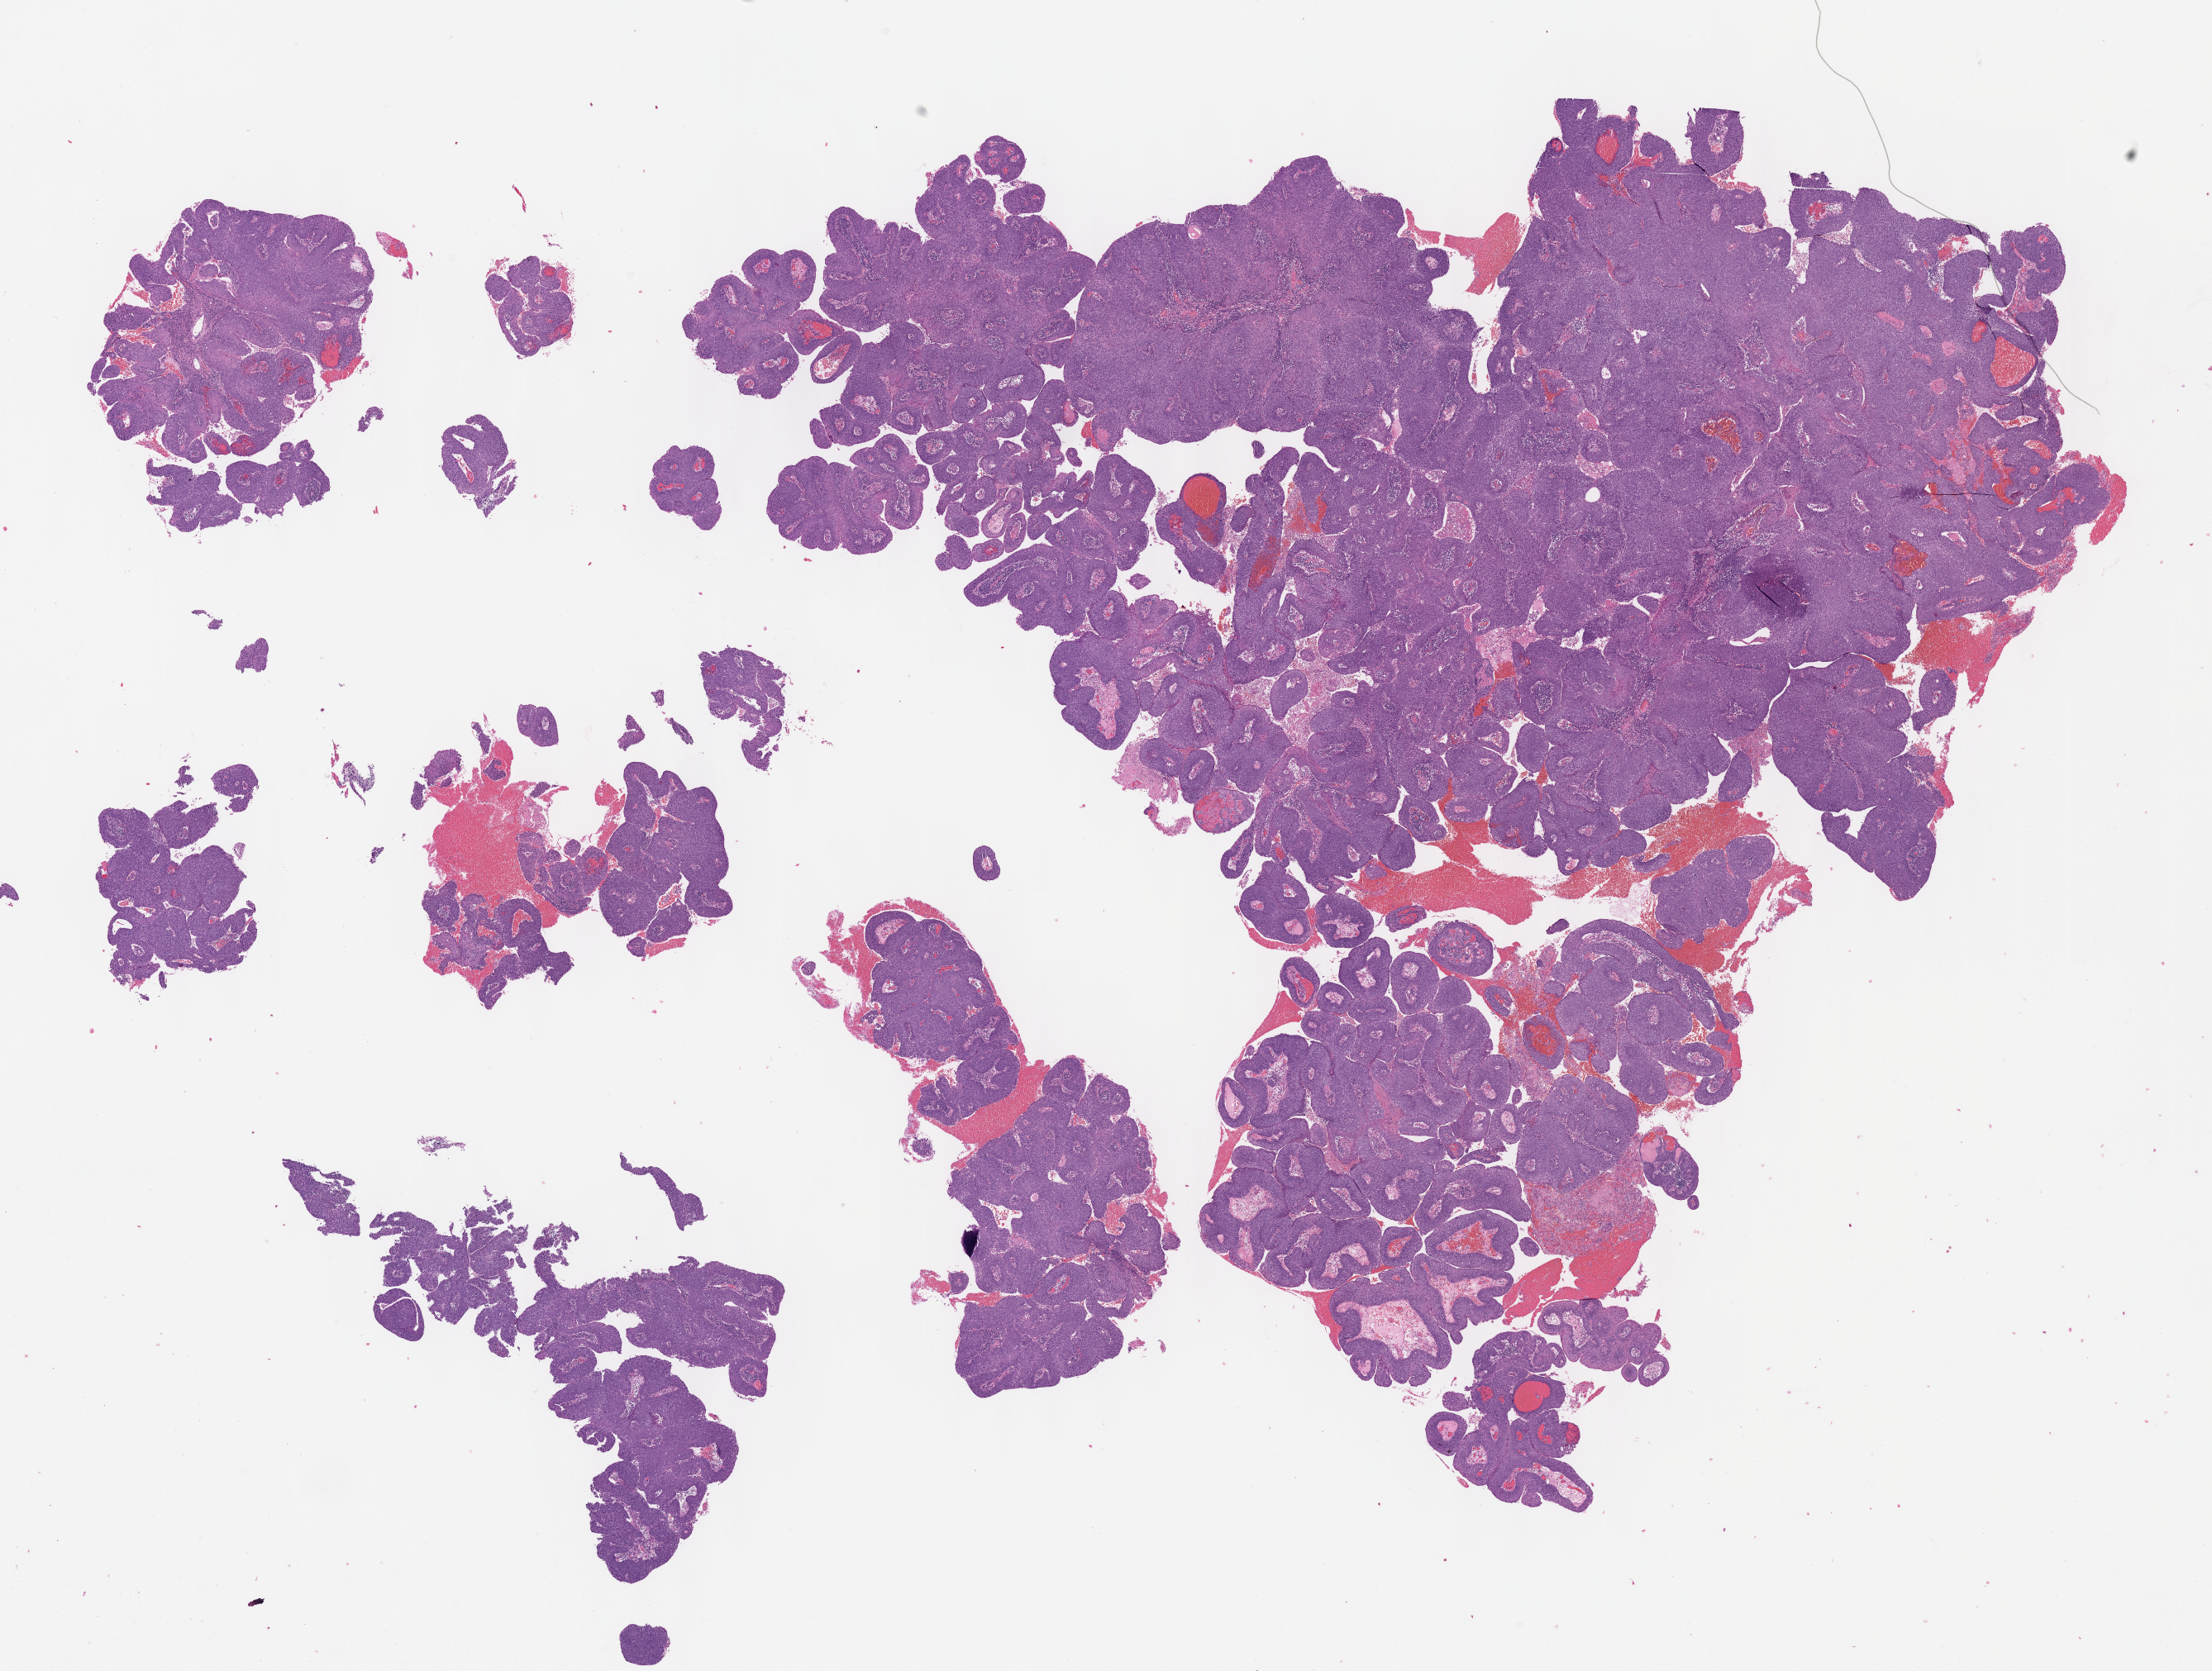
Whole-slide histology image, H&E — low-resolution overview of the scanned area, about 21.6 x 16.3 mm (acquisition: 40x scan), formalin-fixed paraffin-embedded (FFPE) diagnostic section, sample: primary tumour, cervix. Female patient; age at initial diagnosis 43 years. Histologic grade: GX (grade cannot be assessed).
• FIGO stage: IB2
• histologic diagnosis: Squamous cell carcinoma, NOS (cervix uteri)